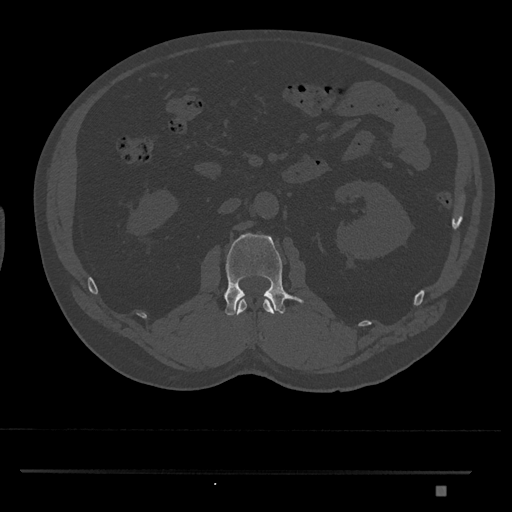
CT including the spine, one axial slice; position 771 of 1134 along the scan axis; bone window (W 1800 / L 400 HU); 0.5 mm slice thickness; 512 × 512 image matrix, field of view 429 × 429 mm. Patient: male, 65 years. Case-level facts recorded for this patient, not image findings: primary cancer: prostate.
Outlined on this slice (semi-automatically segmented with operator editing):
- L1 vertebra: bounding box (x1, y1, x2, y2) in pixels: (236, 299, 275, 315)
- L2 vertebra: (224, 233, 304, 316)